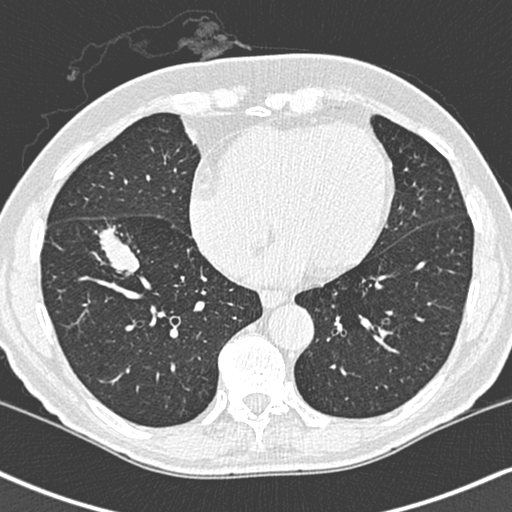
Low-dose screening chest CT, one axial slice; position 99 of 248 along the scan axis; lung window (W 1500 / L -600 HU); 1.3 mm slice thickness; 512 × 512 image matrix, field of view 323 × 323 mm.
Outlined on this slice (manually delineated by an expert):
- lesion 1 (tumor, lower lobe of right lung): bounding box [x1, y1, x2, y2] px = [98, 187, 140, 238]